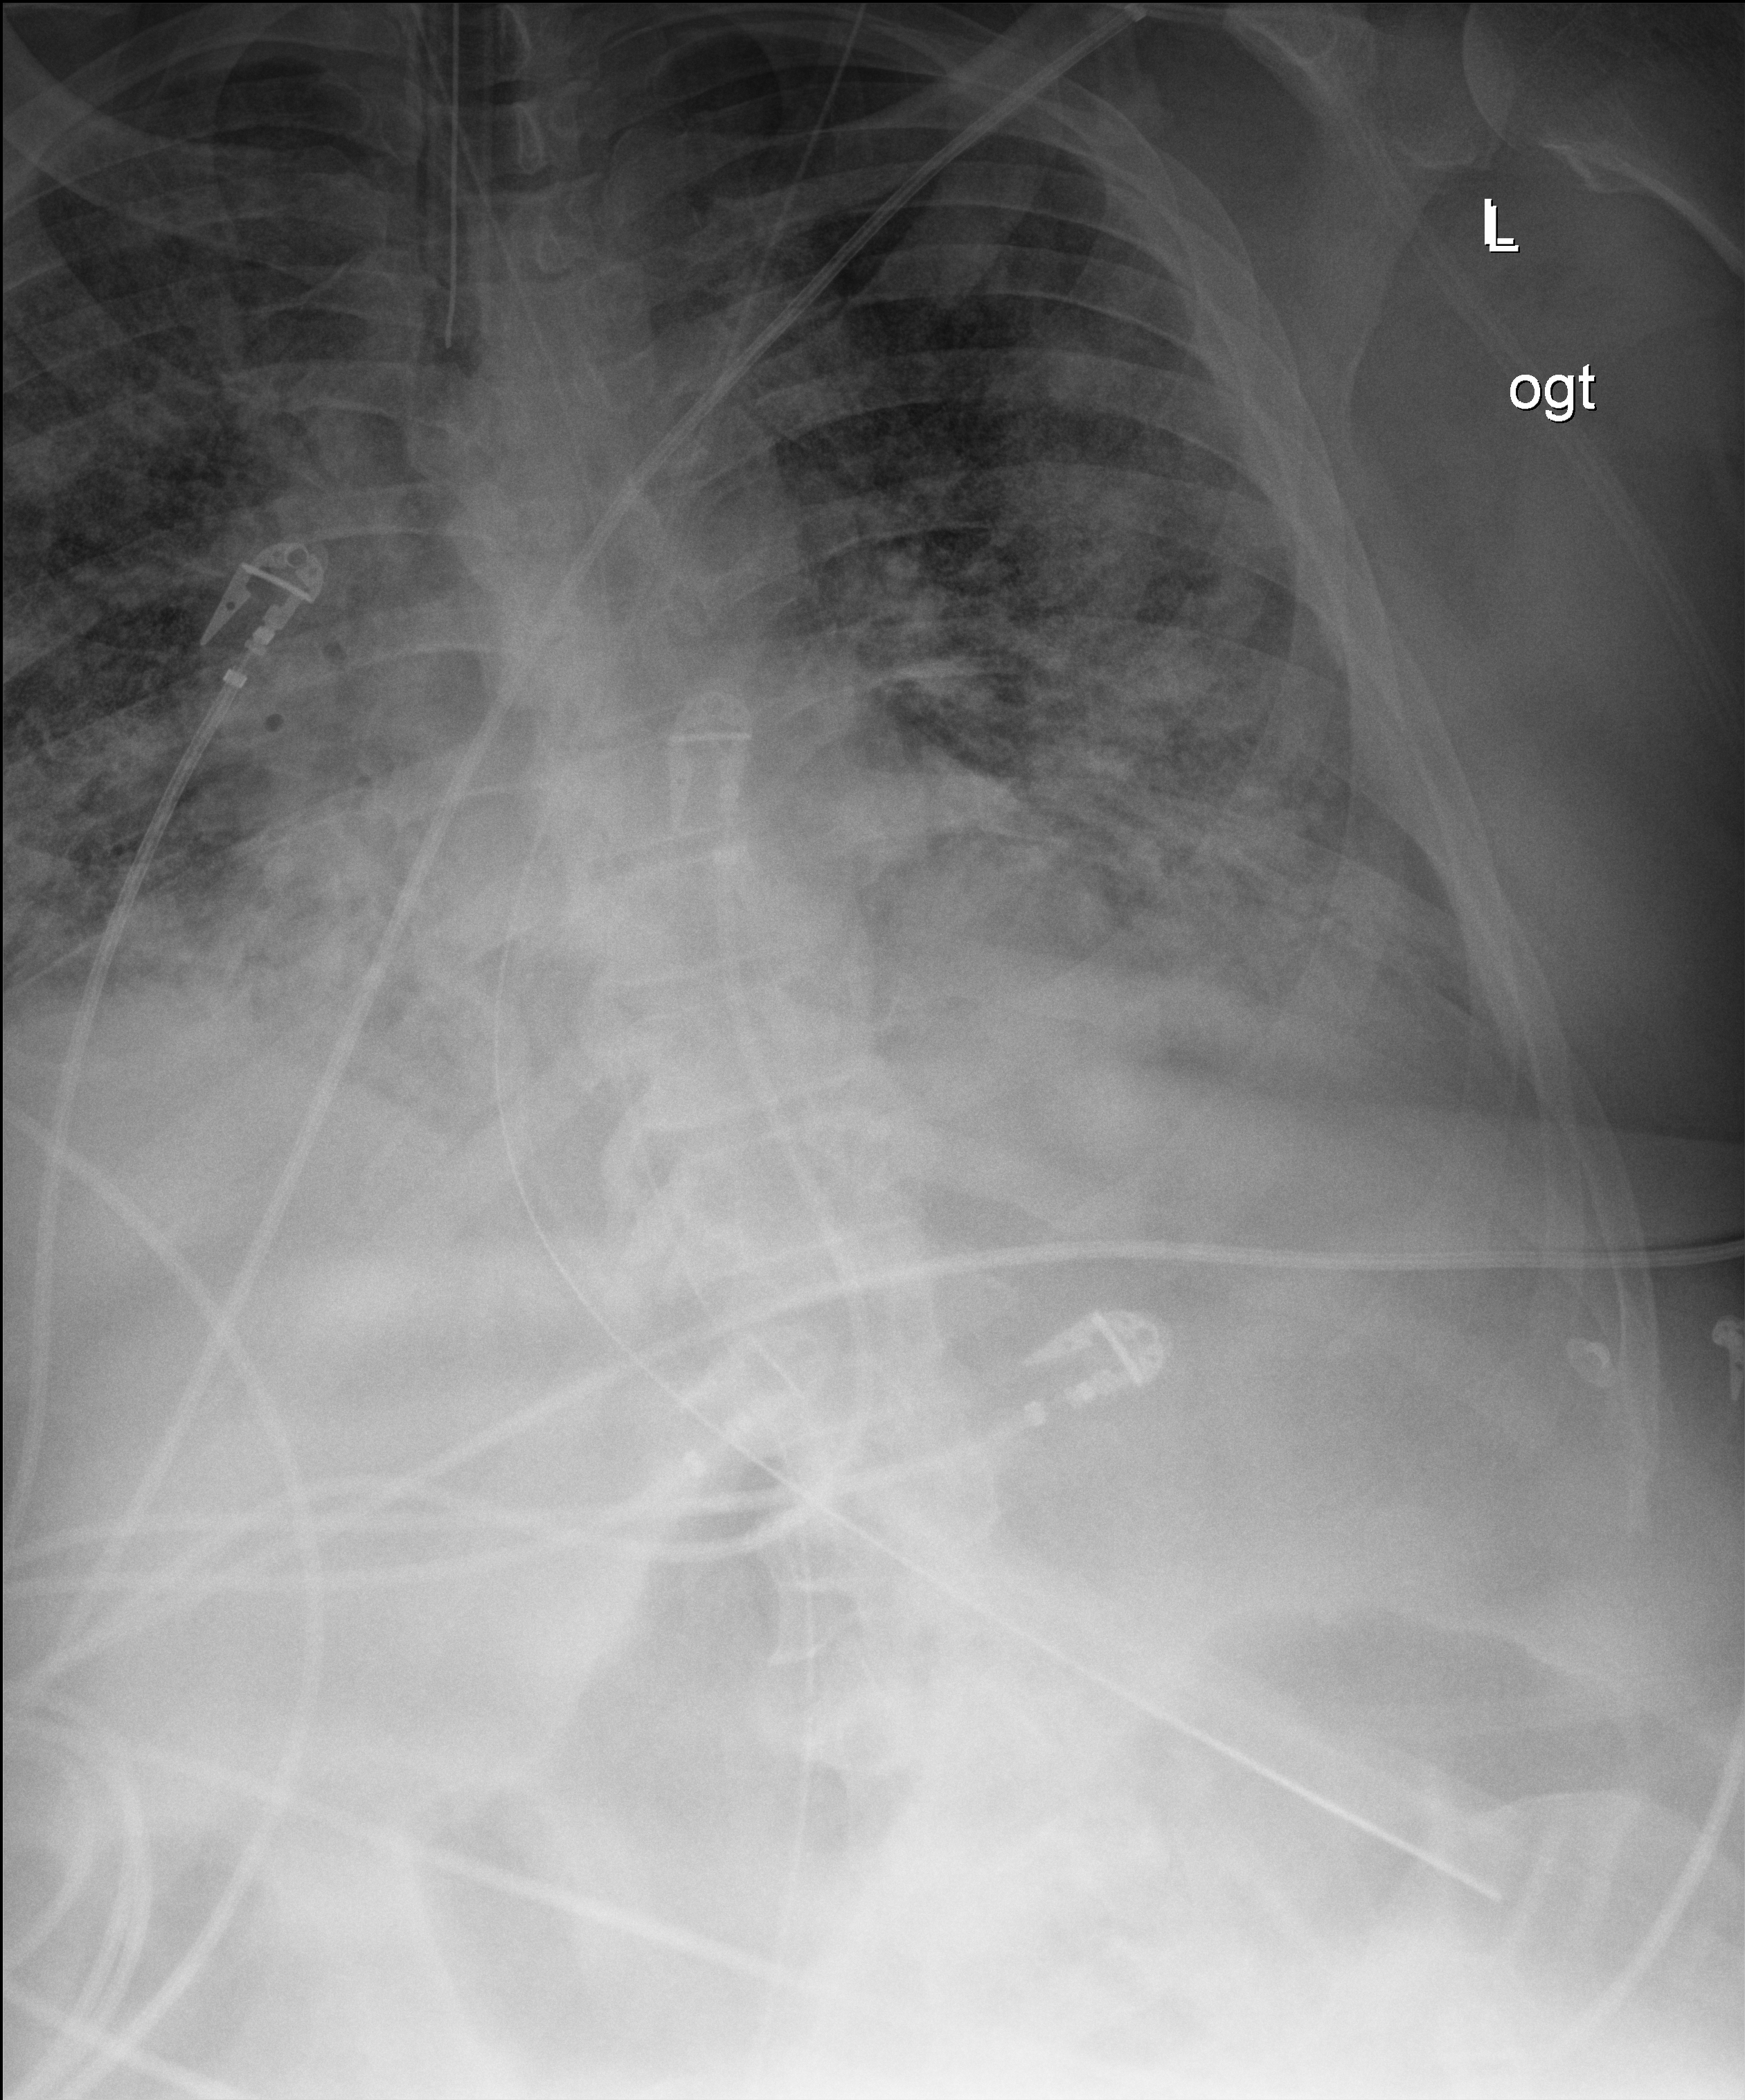
Bedside chest radiograph (digital radiography); anteroposterior (AP) projection. Patient hospitalised with COVID-19; male, aged 60–74 years.
From the hospital-stay record, not from the radiograph (when in the stay this image was taken is not recorded): admitted to intensive care during this hospital stay: yes; length of hospital stay: 34 days.